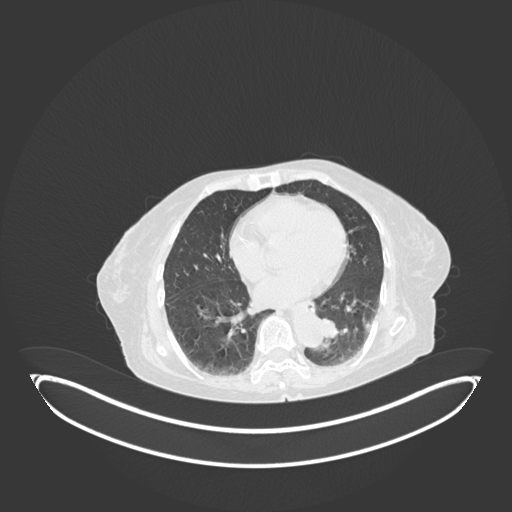
Chest CT, one axial slice. Slice 37 of 189 in the series (ordered by position). Reconstruction kernel B30f. Lung window (W 1500 / L -600 HU). 1 mm slice thickness. 512 × 512 image matrix. Female patient, age 82 years. Case-level facts recorded for this patient, not image findings: clinical TNM (as recorded): T1b N0 M1.
Annotated regions visible in this slice (bounding box drawn by a radiologist):
- lung tumour (recorded histology: adenocarcinoma): bounding box (x1, y1, x2, y2) in pixels: (318, 313, 344, 343)